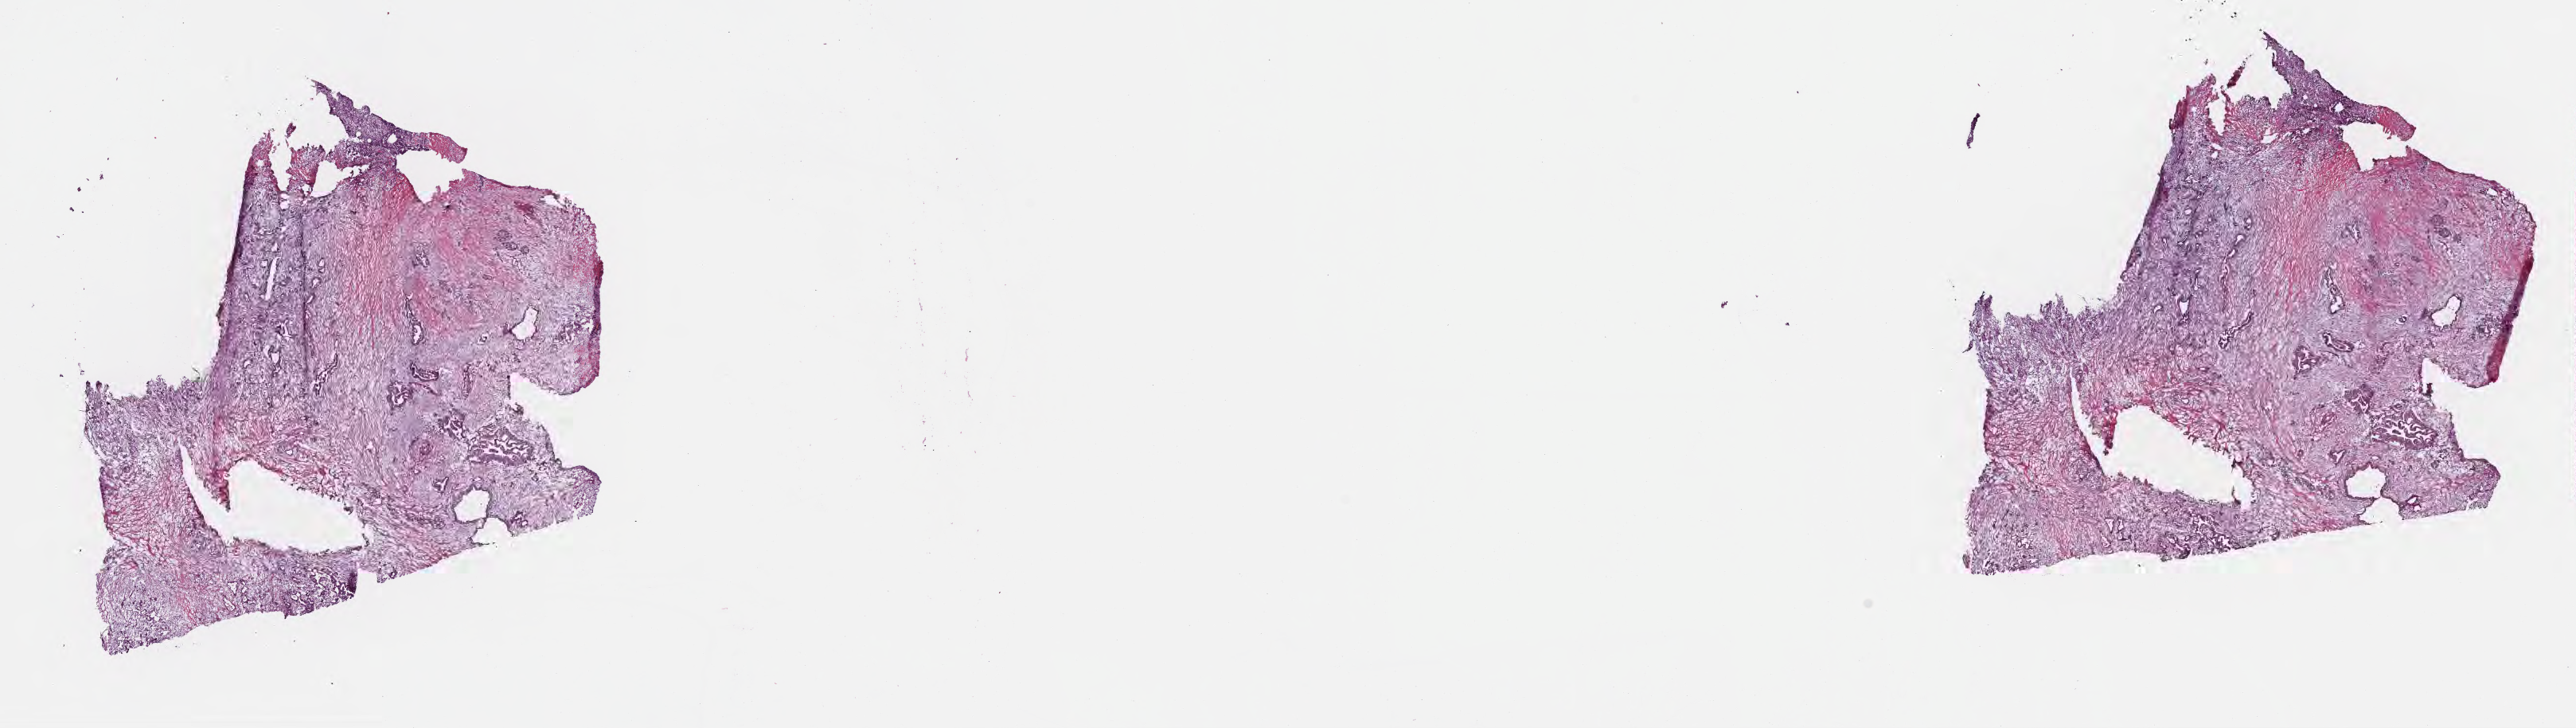
Whole-slide image, hematoxylin and eosin (H&E) stain — whole scanned area (about 26.2 x 7.4 mm) shown as a low-resolution overview, cryosection, specimen: primary tumor, anatomic site: tail of pancreas. Patient: female, age at initial diagnosis 64 years. Tumor grade: G3 (poorly differentiated). Composition of this section per pathologist review: tumor cells 70%, tumor nuclei 70%, stromal cells 26%, necrosis 0%, normal cells 4%. Inflammatory infiltration, as recorded: lymphocyte infiltration 6%, monocyte infiltration 1%, neutrophil infiltration 10%.
Histologic diagnosis: Infiltrating duct carcinoma, NOS. AJCC pathologic stage: Stage III. Section: bottom of the tissue portion.